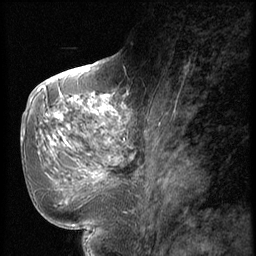
Breast MRI (dynamic contrast-enhanced), one sagittal slice; position 28 of 56 along the scan axis; dynamic contrast-enhanced series, image 2 of 2 at this slice position (ordered by acquisition); 1.5 T; TE 4.2 ms, TR 9 ms; 256 × 256 image matrix, field of view 180 × 180 mm. Female patient, age 51 years. From the clinical record (not read from this slice): setting: breast cancer imaged before/during neoadjuvant chemotherapy; receptor status: triple-negative.
Outlined on this slice (semi-automatic segmentation, software-assisted and operator-edited):
- analysis volume of interest (the breast-tissue region the enhancement analysis was run in; not a lesion): bounding box [x1, y1, x2, y2] px = [60, 98, 147, 197]
- tumour enhancement mask (voxels above the 140 % enhancement threshold inside the analysis volume of interest): [62, 98, 123, 175]